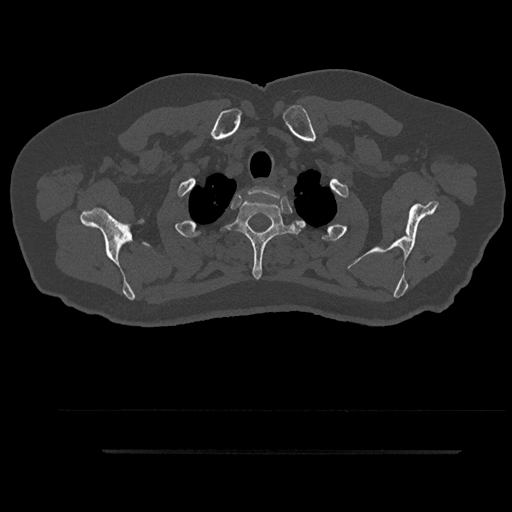
CT including the spine, one axial slice; position 760 of 797 along the scan axis; reconstruction kernel Br40s/3; 120 kVp; bone window (W 1800 / L 400 HU); 0.5 mm slice thickness; 512 × 512 image matrix, field of view 432 × 432 mm. Patient: male, 63 years. From the clinical record (not read from this slice): primary cancer: renal.
Outlined on this slice (semi-automatic segmentation, software-assisted and operator-edited):
- T1 vertebra: bounding box [x1, y1, x2, y2] px = [249, 185, 284, 211]
- T2 vertebra: [226, 199, 304, 279]
- T3 vertebra: [220, 245, 293, 247]